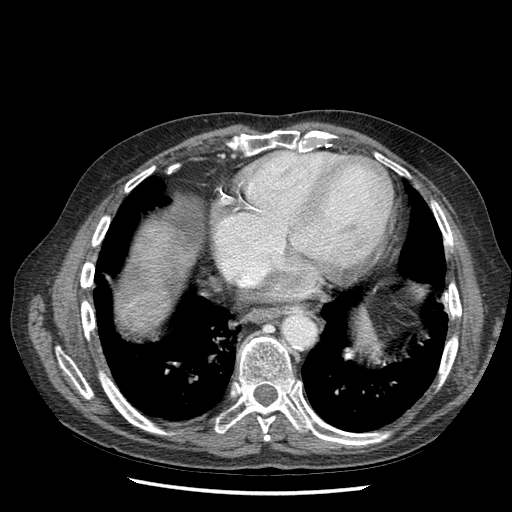
Contrast-enhanced abdominal CT (liver protocol), one axial slice; slice 63 of 67 in the series (ordered by position); reconstruction kernel STANDARD; soft-tissue window (W 400 / L 40 HU); 2.5 mm slice thickness; 512 × 512 image matrix. From the clinical record (not read from this slice): diagnosis: hepatocellular carcinoma (patient treated with transarterial chemoembolisation; whether this scan precedes or follows treatment is not stated here); TNM stage (as recorded): Stage-I; Child-Pugh class: A; tumour differentiation: moderately differentiated.
Outlined on this slice (semi-automatic segmentation, software-assisted and operator-edited):
- liver parenchyma outside the tumour (the mass and vessels are separate outlines, so this box may not span the whole liver): bounding box [x1, y1, x2, y2] px = [134, 234, 170, 316]
- mass: [132, 306, 151, 326]